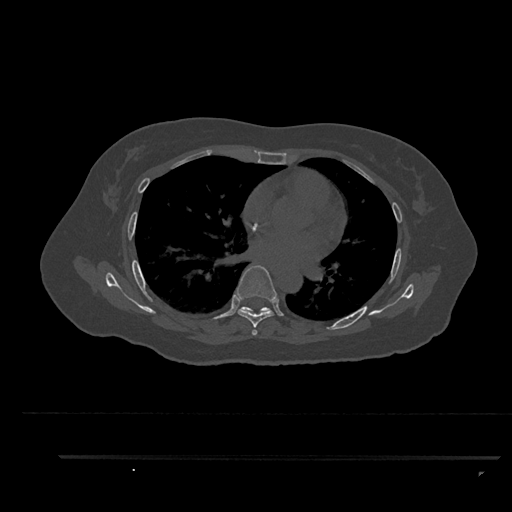
CT including the spine, one axial slice; position 546 of 797 along the scan axis; reconstruction kernel Br40s/3; 120 kVp; bone window (W 1800 / L 400 HU); 0.5 mm slice thickness; 512 × 512 image matrix. Female patient, age 44 years. Case-level facts recorded for this patient, not image findings: primary cancer: renal; vertebrae with lytic lesions (as recorded): L1.
Structures marked on this image (semi-automatically segmented with operator editing):
- T6 vertebra: bounding box [x1, y1, x2, y2] px = [235, 265, 277, 335]
- T7 vertebra: [243, 306, 272, 314]